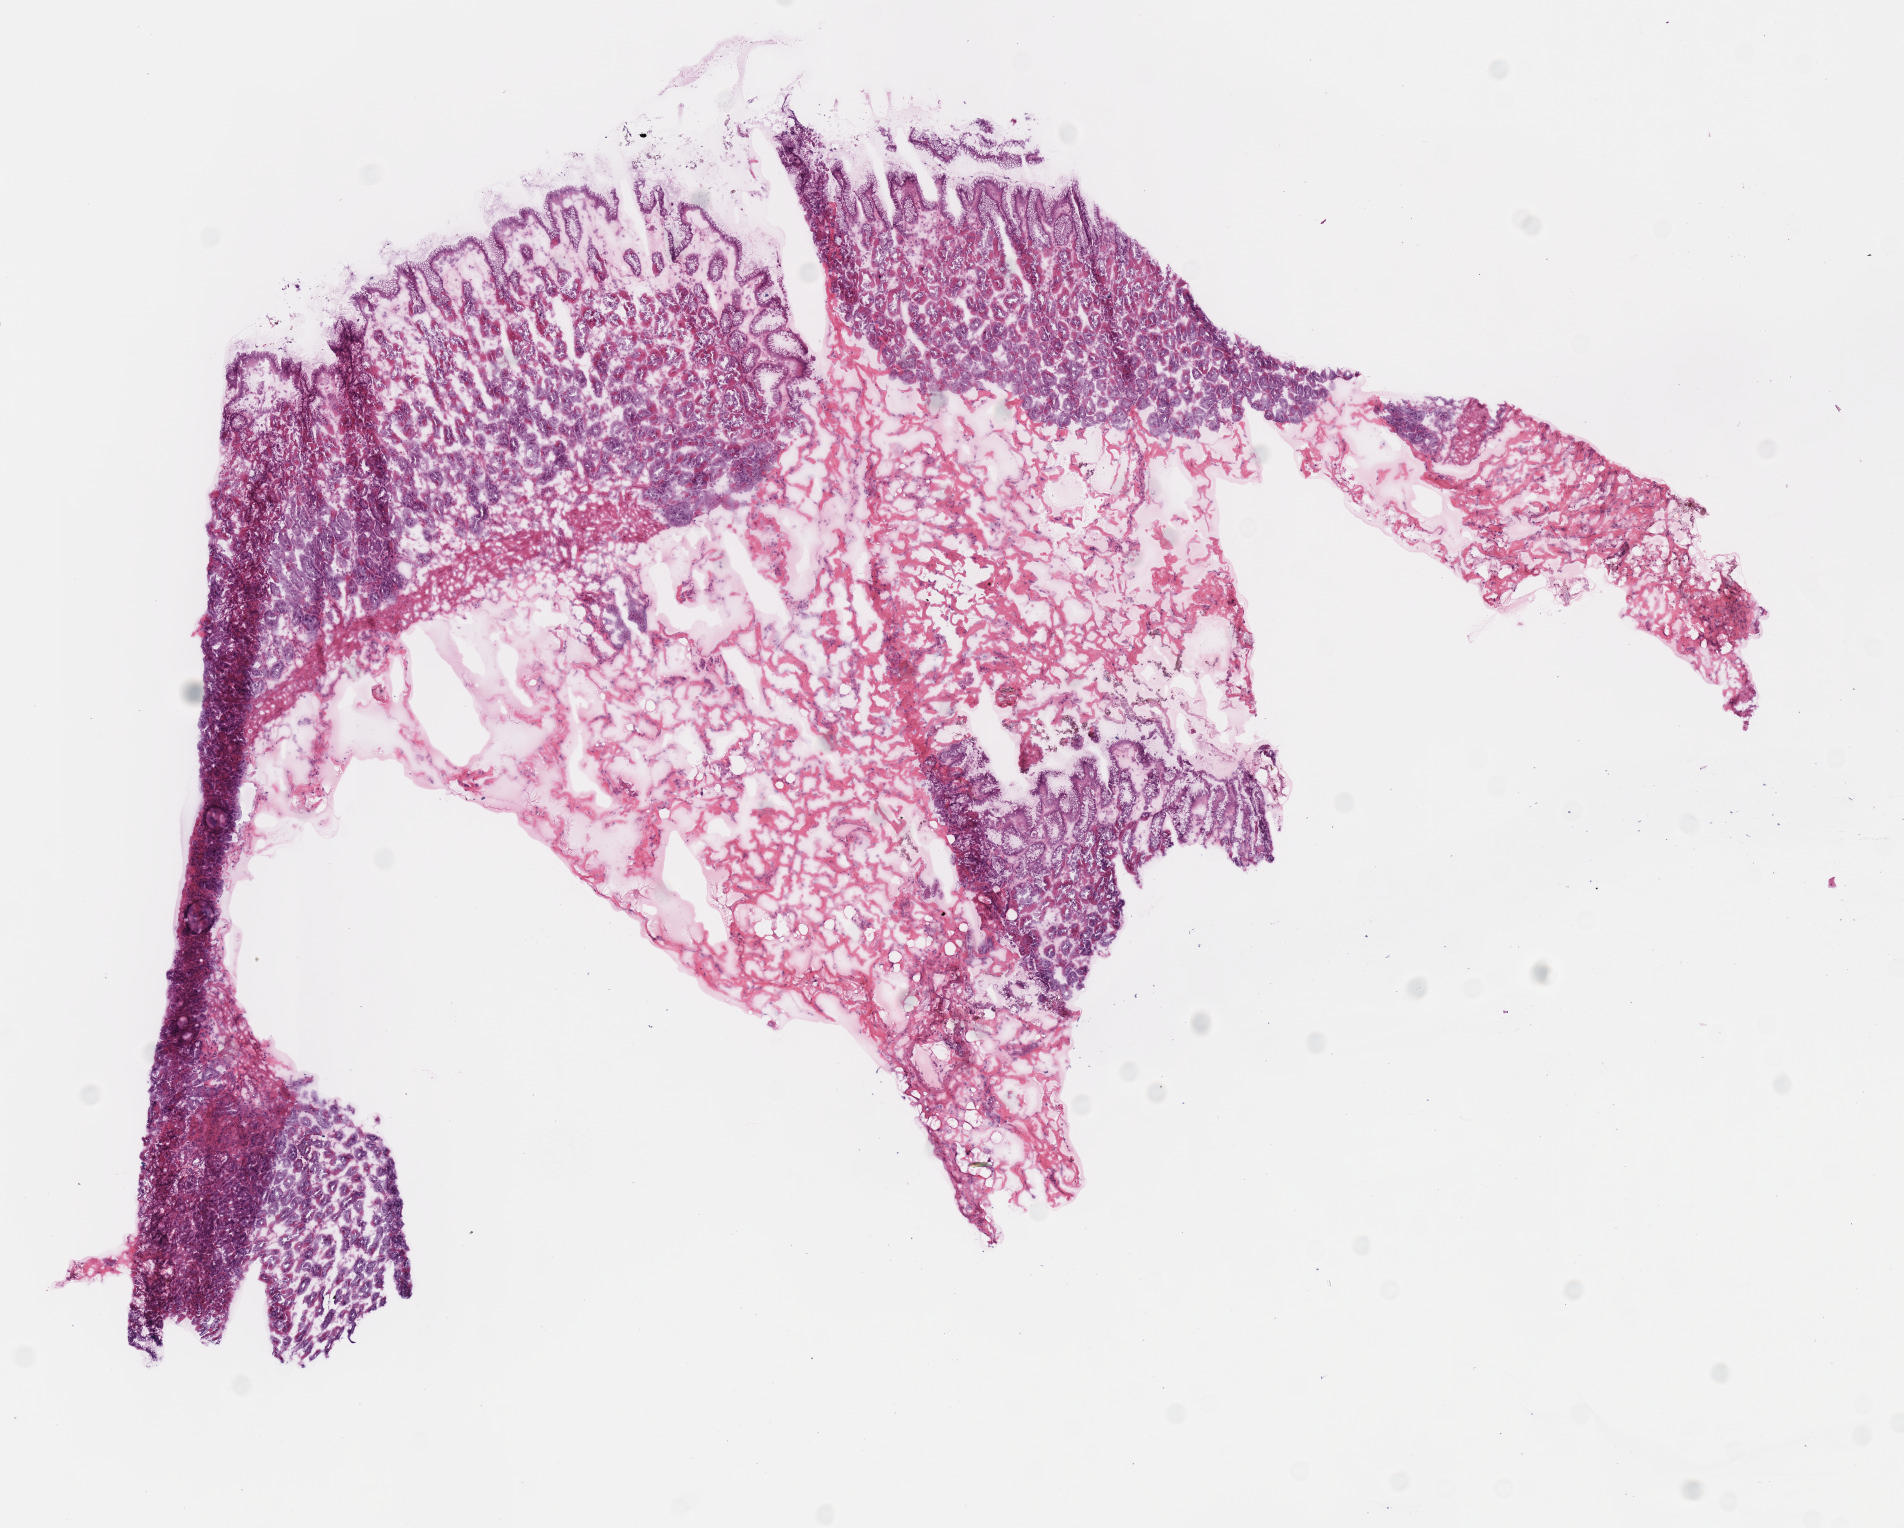
Digitized Hematoxylin and eosin (H&E) stained tissue section (whole slide) — a low-resolution overview of the entire scanned area, about 7.5 x 6.0 mm (slide scanned at 40x). Frozen section. Solid tissue normal (non-tumour tissue) sample from the stomach. Male, age 59 years at initial diagnosis. Inflammatory infiltration, as recorded: lymphocyte infiltration 5%, monocyte infiltration 0%, neutrophil infiltration 0%.
* this section: solid tissue normal sample (biorepository sample class)
* patient diagnosis: Carcinoma, diffuse type (cardia, NOS)